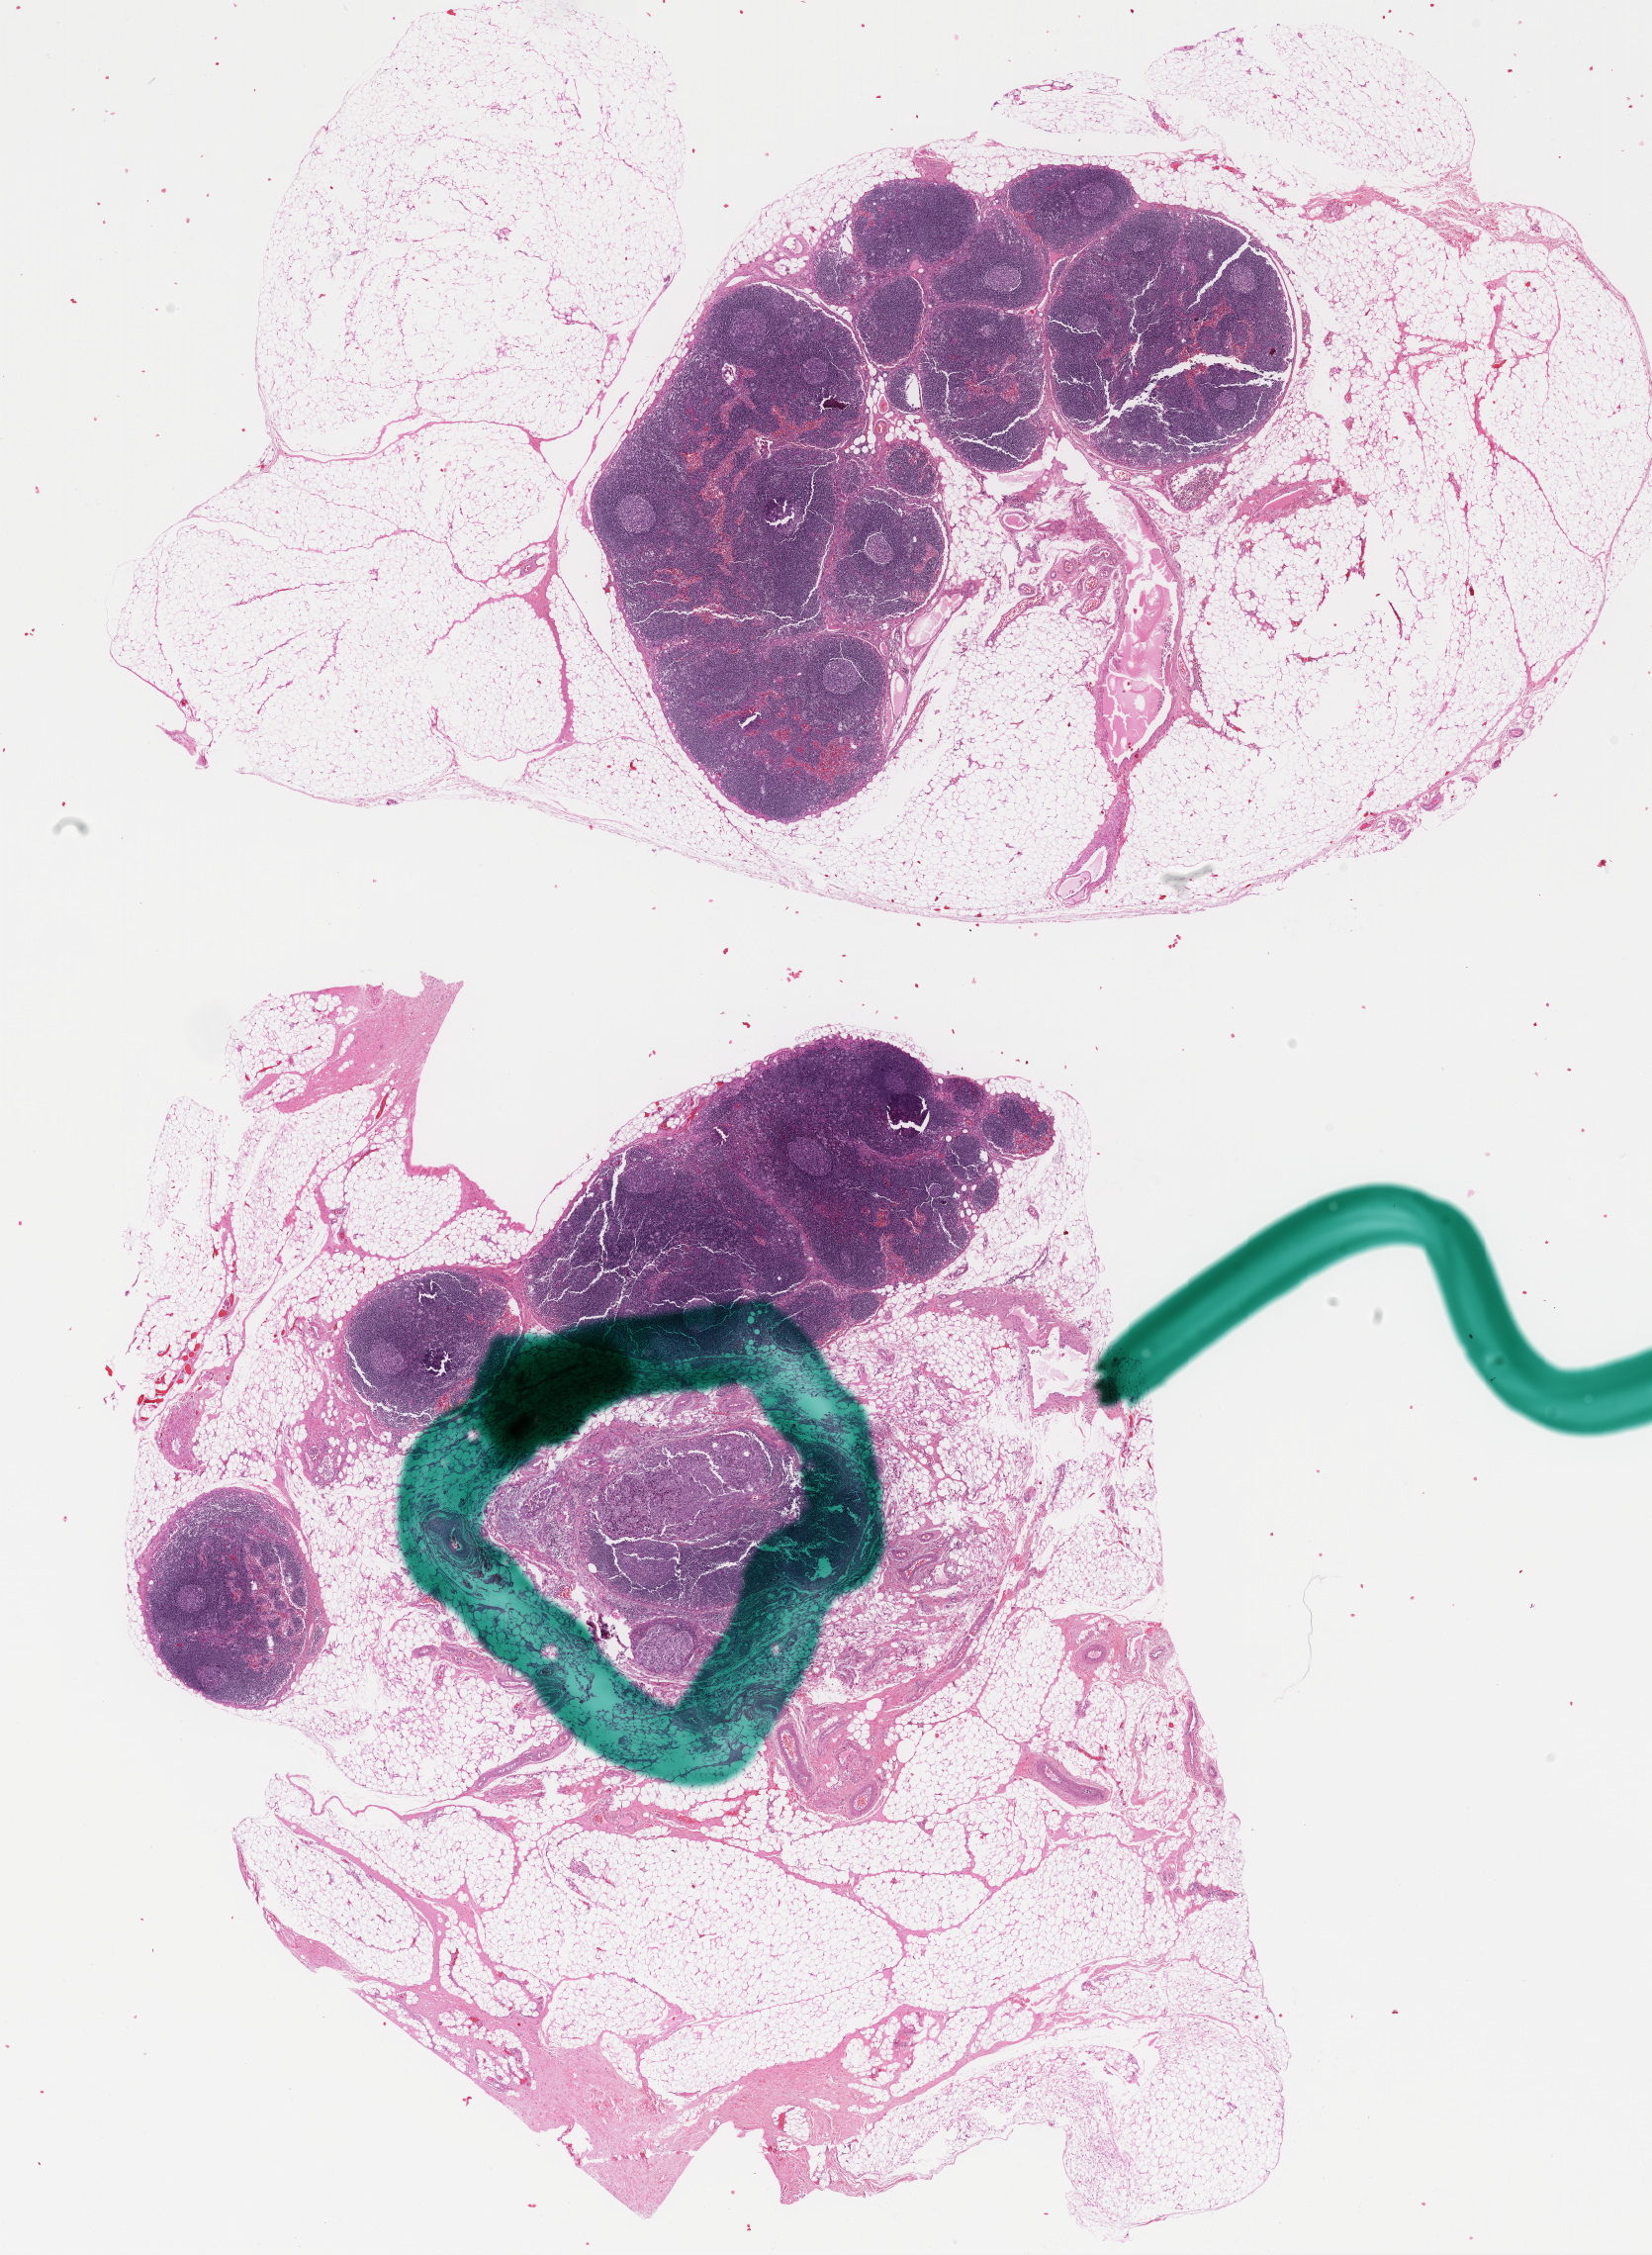
Digitized H&E-stained tissue section (whole slide), whole scanned area (about 13.5 x 18.4 mm) shown as a low-resolution overview, formalin-fixed paraffin-embedded (FFPE) diagnostic section, metastatic tumour sample. Patient: female, age at initial diagnosis 15 years.
This section: metastatic tumour tissue. Patient diagnosis: Malignant melanoma, NOS.